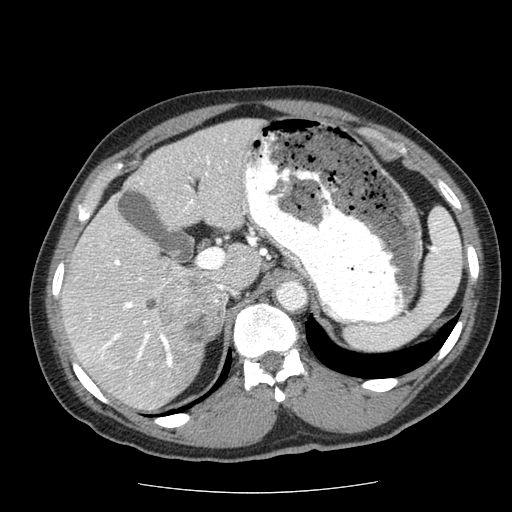
Contrast-enhanced abdominal CT (liver protocol), one axial slice. Position 36 of 85 along the scan axis. 120 kVp. Soft-tissue window (W 400 / L 40 HU). 2.5 mm slice thickness. 512 × 512 image matrix, field of view 360 × 360 mm. Case-level facts recorded for this patient, not image findings: diagnosis: hepatocellular carcinoma (patient treated with transarterial chemoembolisation; whether this scan precedes or follows treatment is not stated here); TNM stage (as recorded): Stage-IIIA; Child-Pugh class: A; tumour nodularity: multinodular.
Outlined on this slice (semi-automatic segmentation, software-assisted and operator-edited):
- abdominal aorta: bounding box (x1, y1, x2, y2) in pixels: (278, 281, 306, 309)
- liver parenchyma outside the tumour (the mass and vessels are separate outlines, so this box may not span the whole liver): (62, 118, 263, 410)
- mass: (143, 273, 224, 341)
- liver vessels: (70, 156, 245, 369)